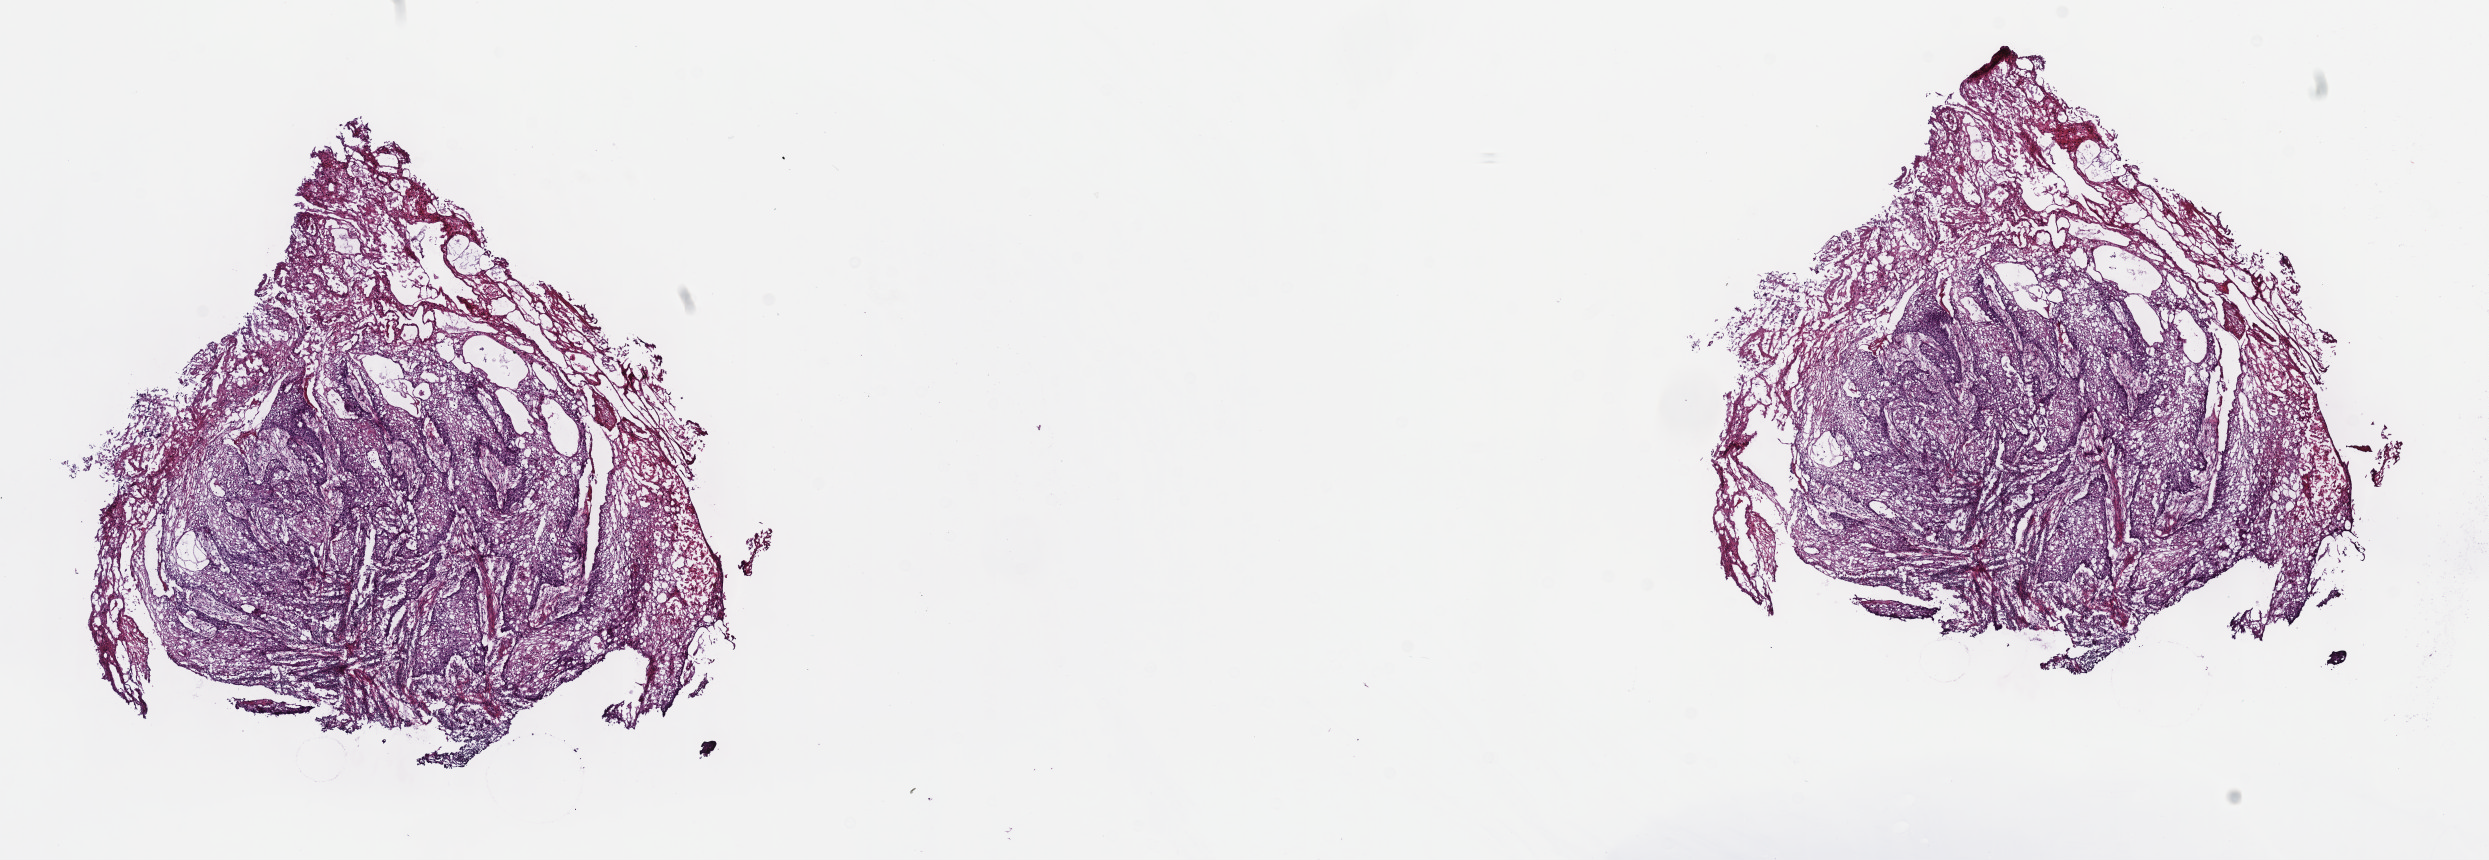
Whole-slide histology image, H&E-stained, shown as a low-resolution overview of the whole scanned area (about 20.1 x 7.0 mm, acquisition: 40x scan). Frozen section. Esophagus, primary tumour sample. Patient: female, age at initial diagnosis 58 years. Histologic grade: G1 (well differentiated). Pathologist review of this section (percent, as recorded): tumour cells 70%, tumour nuclei 70%, normal cells 0%, stromal cells 30%, necrosis 0%. Infiltration values recorded for this section: lymphocyte infiltration 40%, monocyte infiltration 20%, neutrophil infiltration 20%.
AJCC pathologic stage: IB (7th edition). Lymph nodes positive (case pathology): 0 of 39 examined. Diagnosis: Squamous cell carcinoma, NOS (lower third of esophagus).